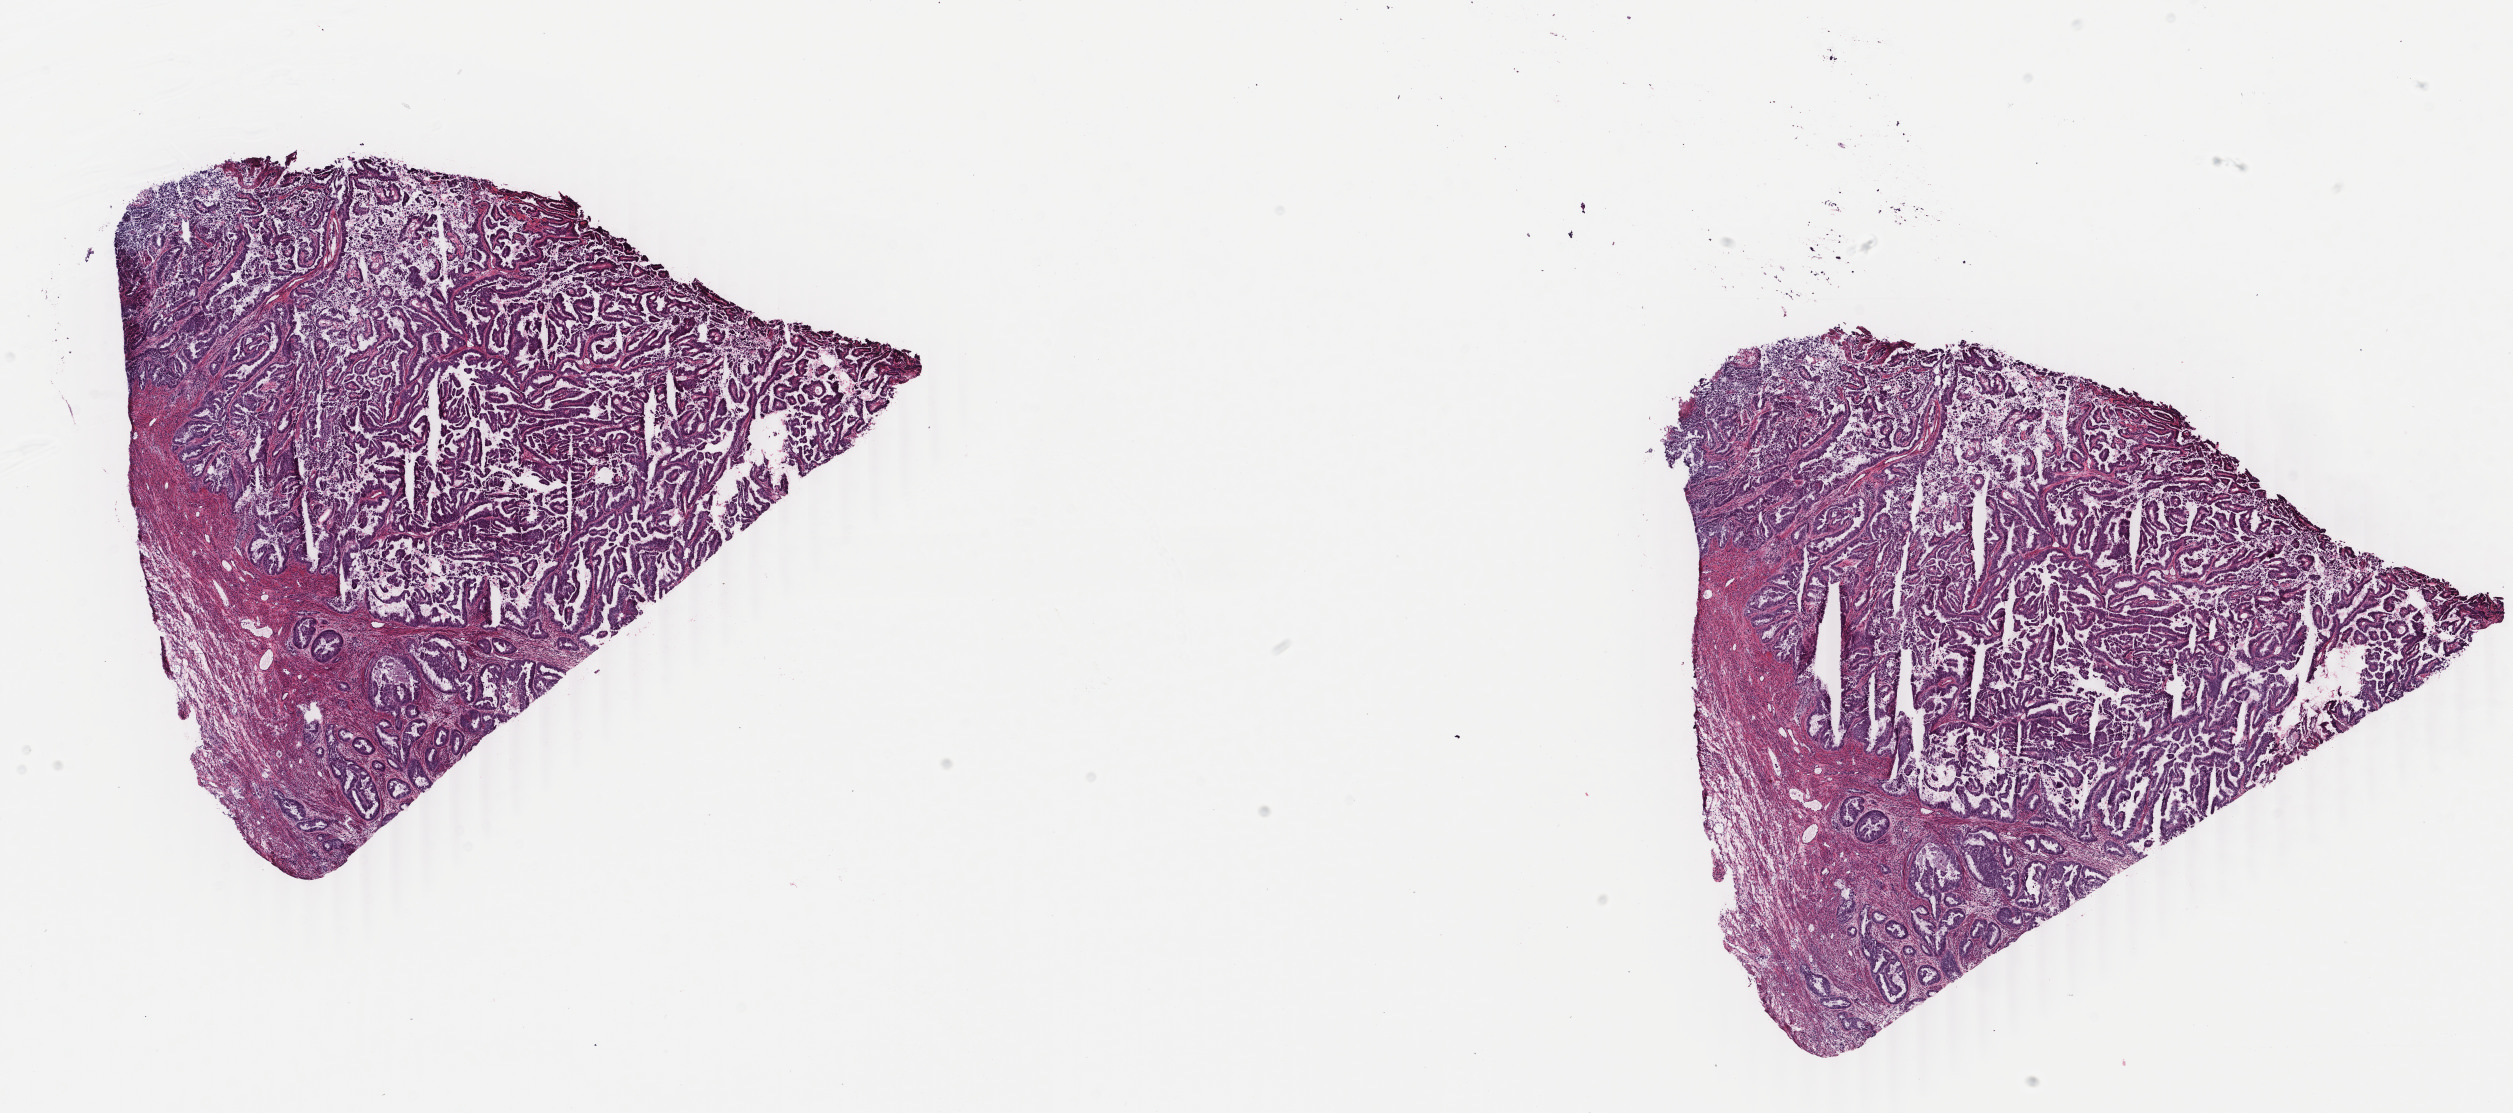
Digitized Hematoxylin and eosin (H&E) stained tissue section (whole slide), shown as a low-resolution overview of the whole scanned area (about 20.0 x 8.9 mm); frozen section from the bottom of the tissue portion; primary tumour sample from the uterus. Patient sex: female. Histologic grade: G2 (moderately differentiated). Slide review estimates, as recorded: tumour cells 50%, tumour nuclei 70%, normal cells 20%, stromal cells 10%, necrosis 20%. Inflammatory infiltration, as recorded: lymphocyte infiltration 20%, monocyte infiltration 0%, neutrophil infiltration 20%.
FIGO stage: IB. Histologic diagnosis: Endometrioid adenocarcinoma, NOS (endometrium).